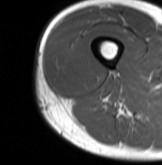
MRI of an extremity soft-tissue mass, one axial slice. Position 22 of 61 along the scan axis. MR volume resampled by the dataset authors to the PET/CT grid (not the native acquisition matrix). 162 × 165 image matrix, field of view 158 × 161 mm. Male patient. From the clinical record (not read from this slice): histological type: poorly differentiated synovial sarcoma; grade: high; site of the primary tumour: right buttock.
Structures marked on this image (expert contour drawn on MRI and transferred to this co-registered scan by the dataset authors):
- gross tumour volume including surrounding oedema: bounding box [x1, y1, x2, y2] px = [52, 42, 97, 94]